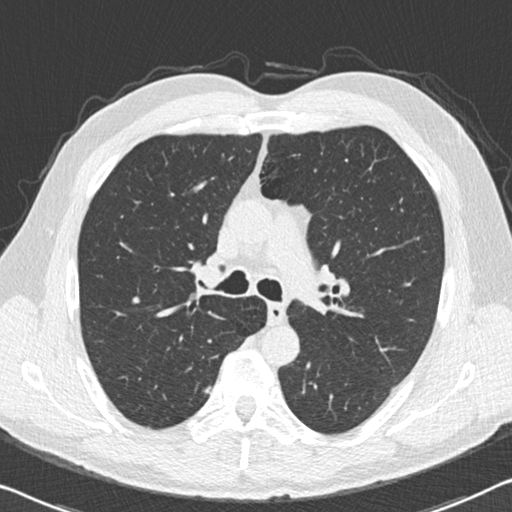
Axial slice from a low-dose chest CT screening exam. Second screening round (one year after baseline). Lung window (W 1500 / L -600 HU). Slice 62 of 179 in the series. Male, age 55 years at enrolment. Current smoker at enrolment.
- Expert-annotated lung lesion, bounding box (x1, y1, x2, y2) in pixels: (193, 375, 223, 406).
- Screening reader's record for this exam: no non-calcified nodule ≥4 mm recorded.
- Official screen result: negative screen, minor abnormalities not suspicious for lung cancer.
- Participant outcome: lung cancer diagnosed 641 days after this screen — adenocarcinoma, NOS, right upper lobe, poorly differentiated (G3), stage IA (AJCC 6th edition), 15 mm at pathology.